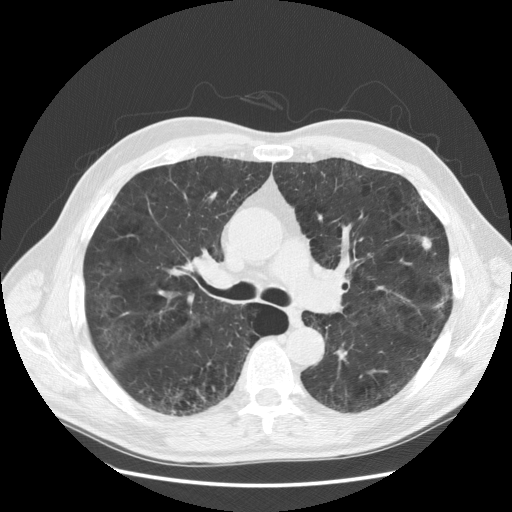
Low-dose screening chest CT, axial slice, third screening round (two years after baseline), lung window (W 1500 / L -600 HU), 2.5 mm slice thickness, slice 69 of 163 in the series, 512 × 512 image matrix, field of view 380 × 380 mm. Male participant, aged 58 years at enrolment.
• Lesion marked by an expert reader, bounding box <408,223,448,261> (left, top, right, bottom; pixels).
• The exam's reader record, not a measurement of the box and not confirmed to be the same lesion: non-calcified nodule or mass ≥4 mm, left upper lobe, 9 × 8 mm, poorly defined margins, soft tissue attenuation, pre-existing on the prior screen: no.
• Later outcome: lung cancer diagnosed 53 days after this screen — adenocarcinoma, NOS, left upper lobe, stage IA (AJCC 6th edition), 9 mm at pathology.